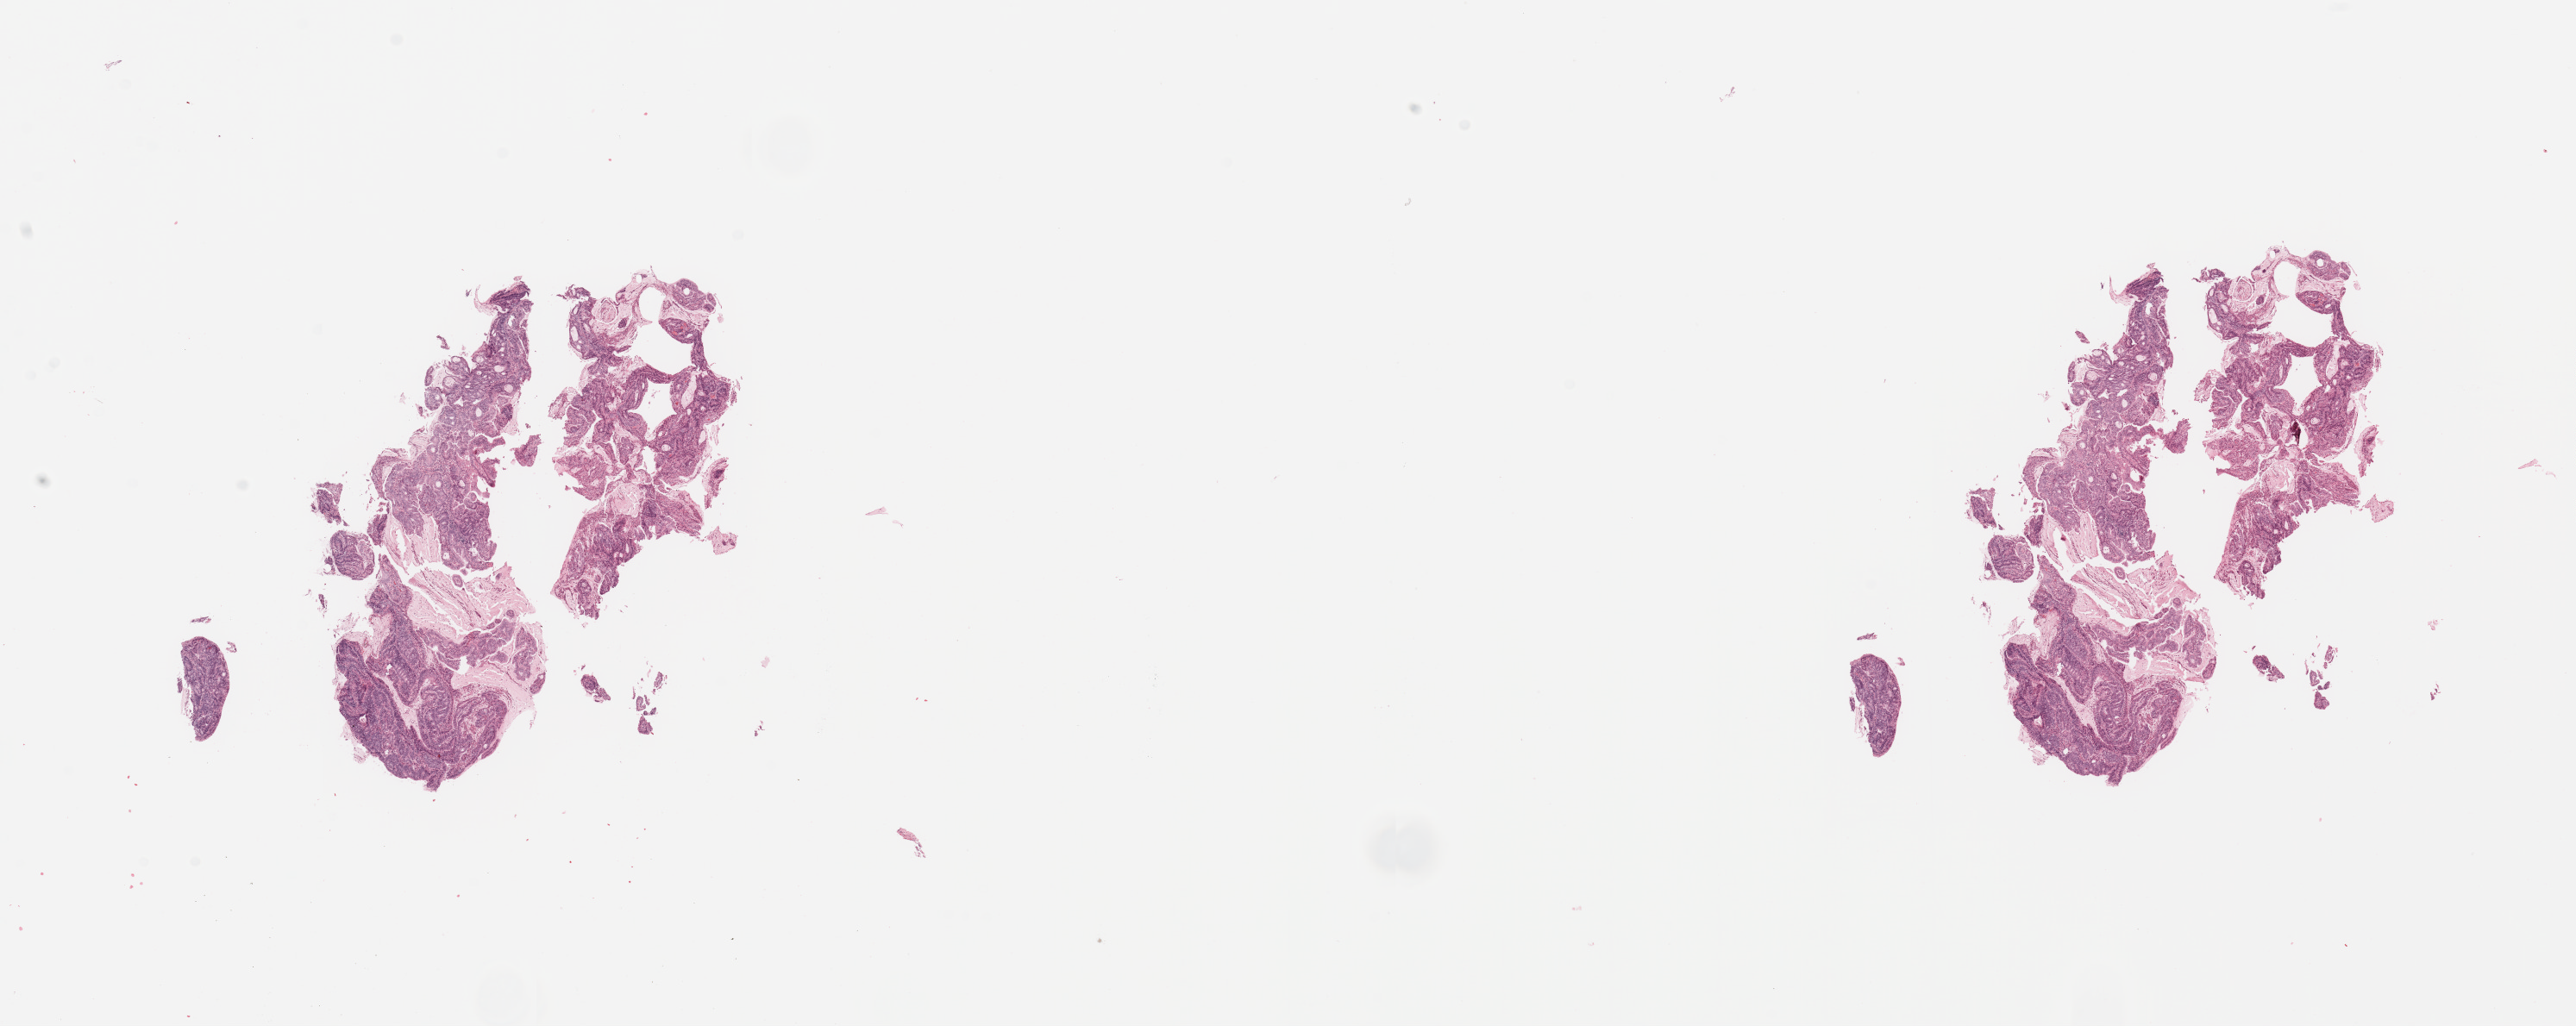
Digitized H&E tissue section (whole slide) — whole scanned area (about 23.6 x 9.4 mm, from a 20x scan) shown as a low-resolution overview, tumour tissue sample, sampled site: uterus. Female, 53 y/o. Histologic grade: G1 (well differentiated). Composition of this section per pathologist review: tumour nuclei 80%, necrosis 0%.
* AJCC pathologic stage: III
* primary tumour site (as recorded): anterior endometrium
* histologic diagnosis: Endometrioid adenocarcinoma, NOS